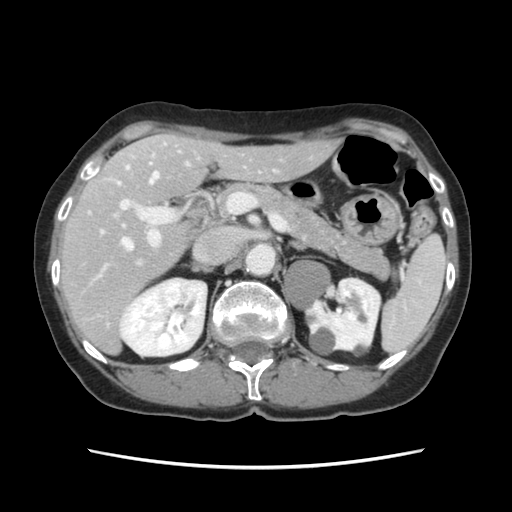
Contrast-enhanced abdominal CT, one axial slice; position 72 of 120 along the scan axis; intravenous contrast given; soft-tissue window (W 400 / L 40 HU); 512 × 512 image matrix, field of view 330 × 330 mm. Female patient, age 70 years. From the clinical record (not read from this slice): diagnosis: colorectal cancer liver metastases, imaged before liver resection; multiple liver metastases: no; largest metastasis: 2.5 cm.
Annotated regions visible in this slice (expert manual segmentation):
- hepatic veins: bounding box <101,155,158,250> (left, top, right, bottom; pixels)
- liver: <61,135,337,352>
- planned liver remnant (the part of the liver to remain after resection): <89,135,337,280>
- portal vein (with intrahepatic branches): <115,144,232,264>